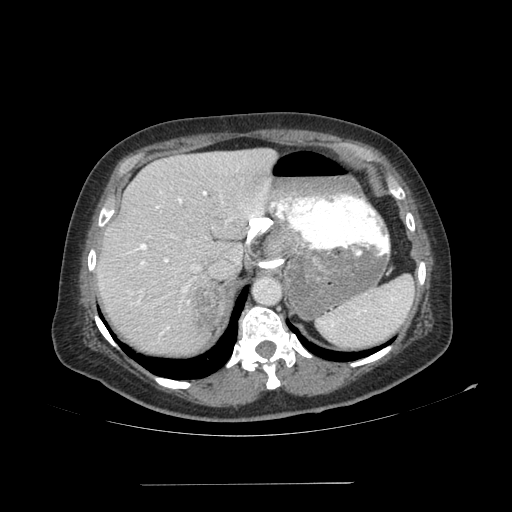
Contrast-enhanced abdominal CT, one axial slice; position 80 of 113 along the scan axis; reconstruction kernel SOFT; soft-tissue window (W 400 / L 40 HU); 512 × 512 image matrix, field of view 440 × 440 mm. Female patient, age 67 years. Case-level facts recorded for this patient, not image findings: diagnosis: adrenocortical carcinoma; tumour side: right adrenal; tumour size at pathology: 9.8 cm; Ki-67 index: 59 %.
Outlined on this slice (semi-automatic segmentation, software-assisted and operator-edited):
- mass: box from (x=187, y=280) to (x=226, y=330) px